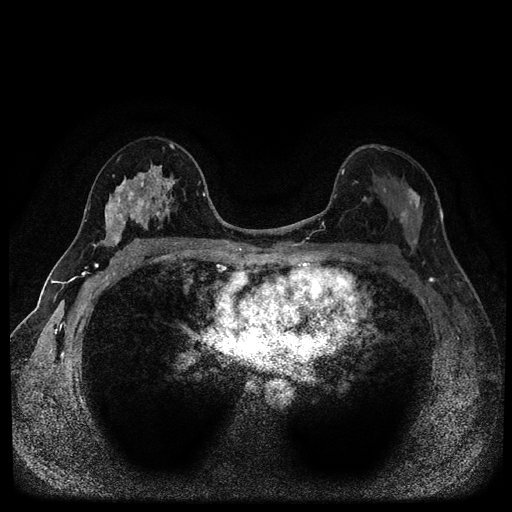
Breast MRI (dynamic contrast-enhanced, multi-phase), one axial slice. Position 59 of 116 along the scan axis. Dynamic contrast-enhanced series, time point 2 of 5 at this slice position (early post-contrast). 1.5 T. TE 2.7 ms, TR 5.4 ms. 2 mm slice thickness. 512 × 512 image matrix, field of view 320 × 320 mm. Patient: female, 49 years.
Structures marked on this image (semi-automatic segmentation, software-assisted and operator-edited):
- breast lesion (labelled benign in the annotation): bounding box [x1, y1, x2, y2] px = [102, 161, 176, 250]